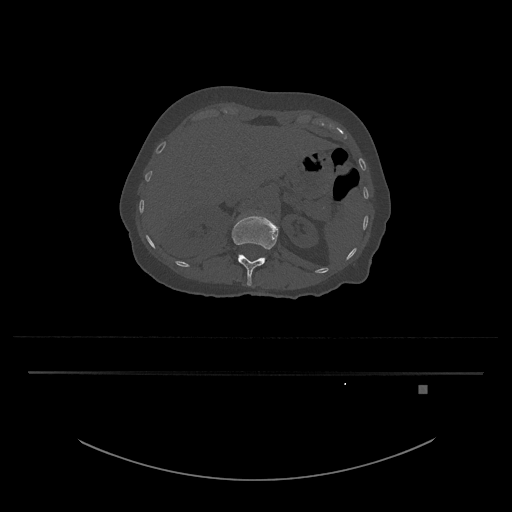
CT including the spine, one axial slice. Position 544 of 797 along the scan axis. Reconstruction kernel Br40s/3. 120 kVp. Bone window (W 1800 / L 400 HU). 0.5 mm slice thickness. 512 × 512 image matrix. Female patient, age 57 years. From the clinical record (not read from this slice): primary cancer: cervical.
Outlined on this slice (semi-automatically segmented with operator editing):
- L1 vertebra: bounding box [x1, y1, x2, y2] px = [232, 216, 279, 286]